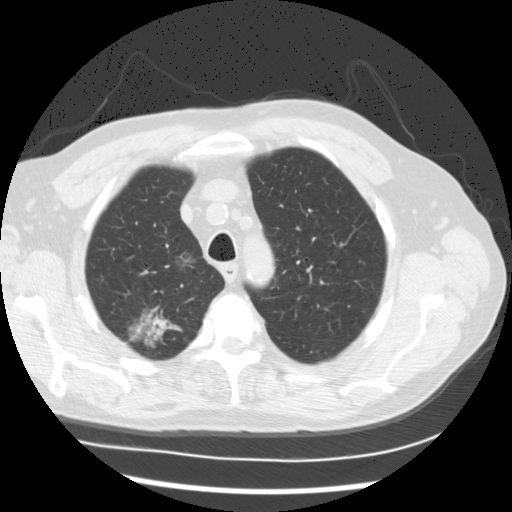
Chest CT (low-dose screening protocol), one axial image; baseline screening round; lung window (W 1500 / L -600 HU); 2.5 mm slice thickness; standard (soft-tissue) reconstruction kernel (STANDARD); 512 × 512 image matrix. Male participant, aged 68 years at enrolment. Current smoker at enrolment.
Expert reader's lesion annotation, bounding box [x1, y1, x2, y2] px = [114, 291, 189, 362]. The screening reader recorded 3 non-calcified nodules or masses ≥4 mm on this exam (right upper lobe, right upper lobe, right lower lobe); which of them this box marks is not recorded. Official screen result: positive, change unspecified: nodule(s) >= 4 mm or enlarging nodule(s), mass(es), or other non-specific abnormalities suspicious for lung cancer.